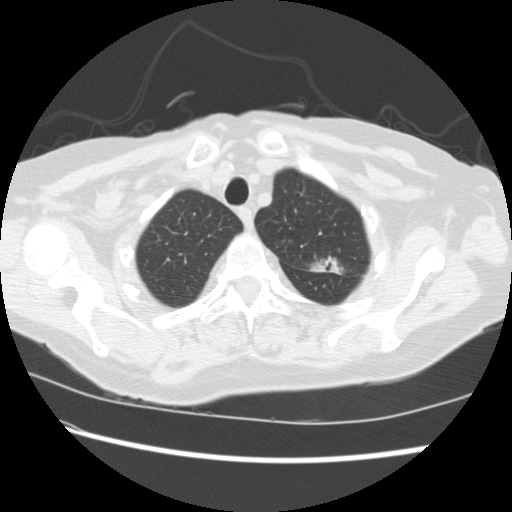
Low-dose screening chest CT, axial slice; baseline annual screen; lung window (W 1500 / L -600 HU); 2.5 mm slice thickness; 512 × 512 image matrix. Female, age 74 years at enrolment. Former smoker at enrolment.
• Expert-annotated lung lesion, bounding box (x1, y1, x2, y2) in pixels: (298, 247, 348, 284).
• The screening reader recorded 2 non-calcified nodules or masses ≥4 mm on this exam (left upper lobe, right lower lobe); which of them this box marks is not recorded.
• Official screen result: positive, change unspecified: nodule(s) >= 4 mm or enlarging nodule(s), mass(es), or other non-specific abnormalities suspicious for lung cancer.
• Participant outcome: lung cancer diagnosed 309 days after this screen — non-small cell carcinoma, left upper lobe, stage IV (AJCC 6th edition).